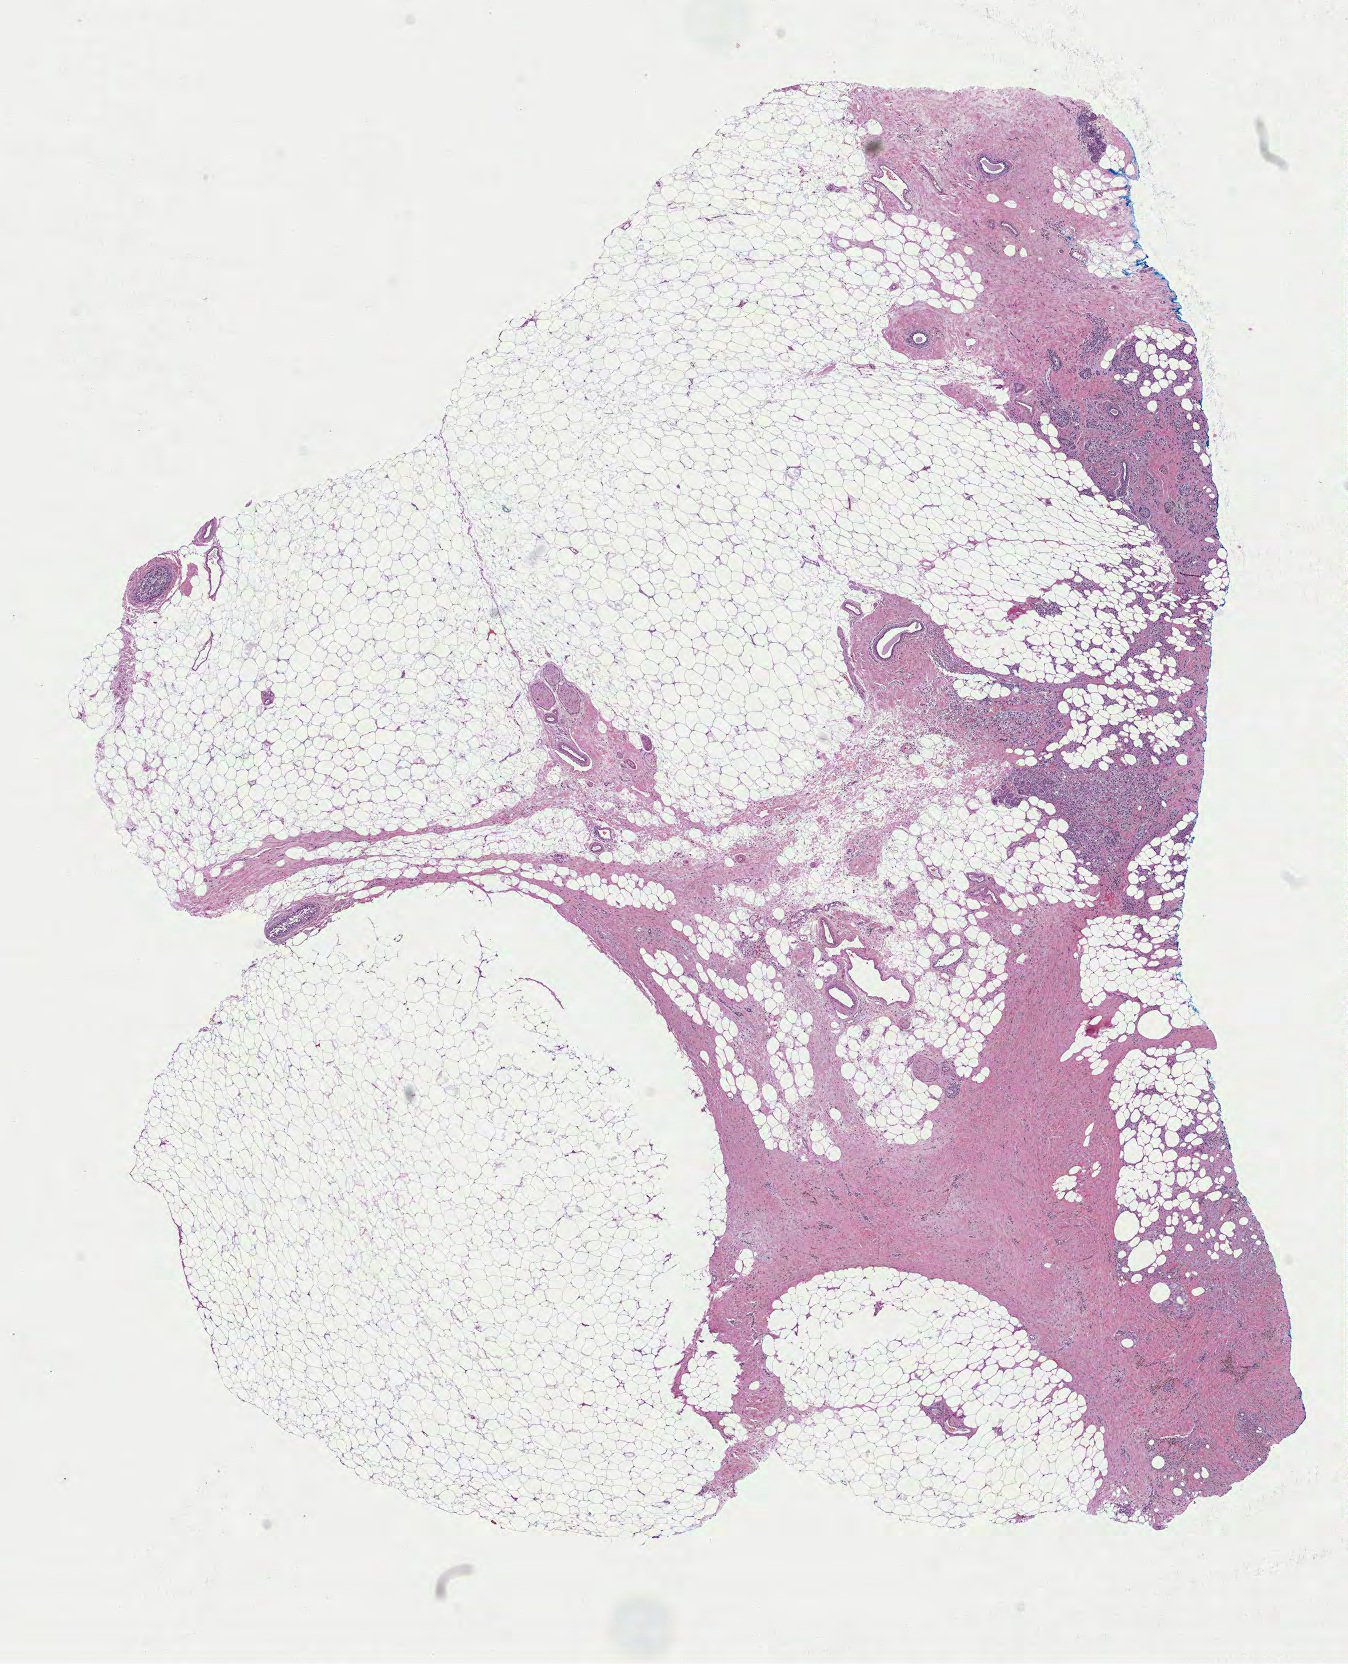
Hematoxylin and eosin (H&E) stained whole-slide image, shown as a low-resolution overview of the whole scanned area (about 10.9 x 13.4 mm, acquisition: 40x scan), FFPE section, sample: primary tumour, breast. Female patient; age at initial diagnosis 72 years.
• AJCC pathologic stage: IA (7th edition)
• laterality: right
• lymph nodes positive (case pathology): 0 of 6 examined
• diagnosis: Infiltrating duct carcinoma, NOS